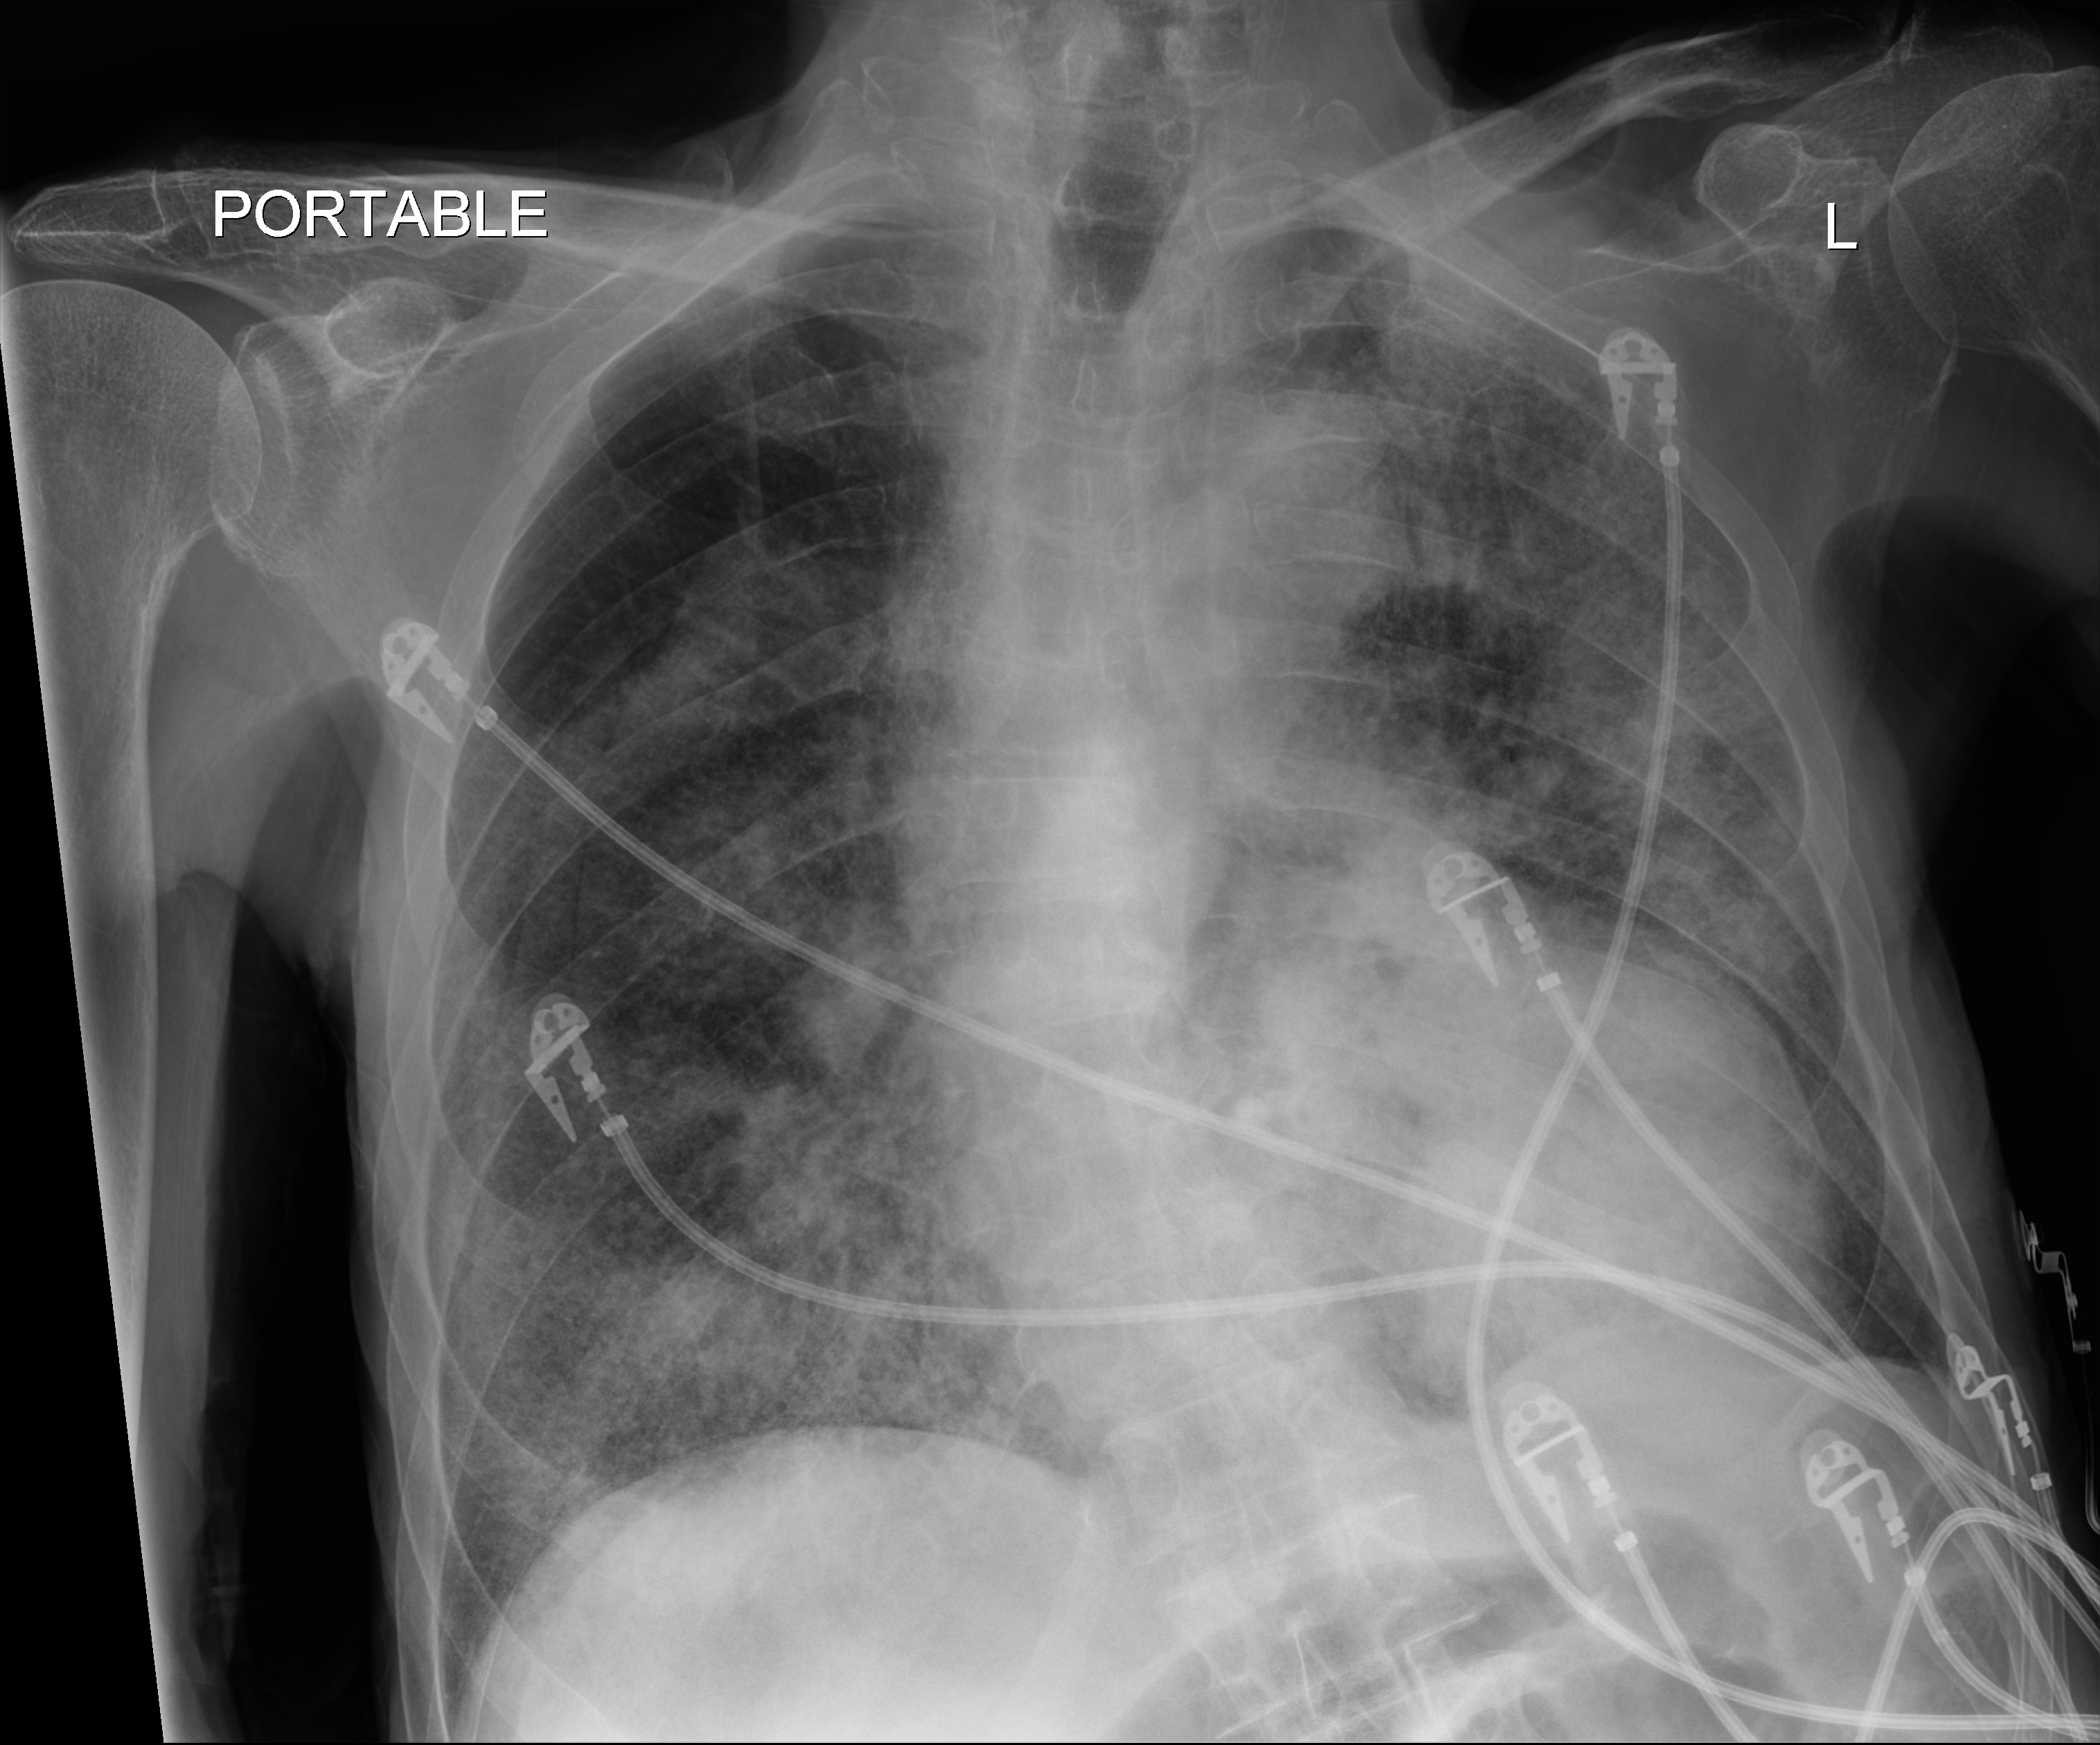
Chest radiograph (digital radiography). Patient hospitalised with COVID-19; male, aged 75–90 years.
From the hospital-stay record, not from the radiograph (when in the stay this image was taken is not recorded):
- other chronic lung disease (admission record): no
- mechanically ventilated during this hospital stay: no